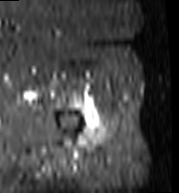
MRI of an extremity soft-tissue mass, one axial slice. Position 96 of 103 along the scan axis. STIR. MR volume resampled by the dataset authors to the PET/CT grid (not the native acquisition matrix). 179 × 193 image matrix, field of view 175 × 188 mm. Female patient. From the clinical record (not read from this slice): histological type: undifferentiated – high grade; grade: high; site of the primary tumour: left thigh.
Annotated regions visible in this slice (expert contour drawn on MRI and transferred to this co-registered scan by the dataset authors):
- gross tumour volume including surrounding oedema: bounding box (x1, y1, x2, y2) in pixels: (86, 117, 105, 136)